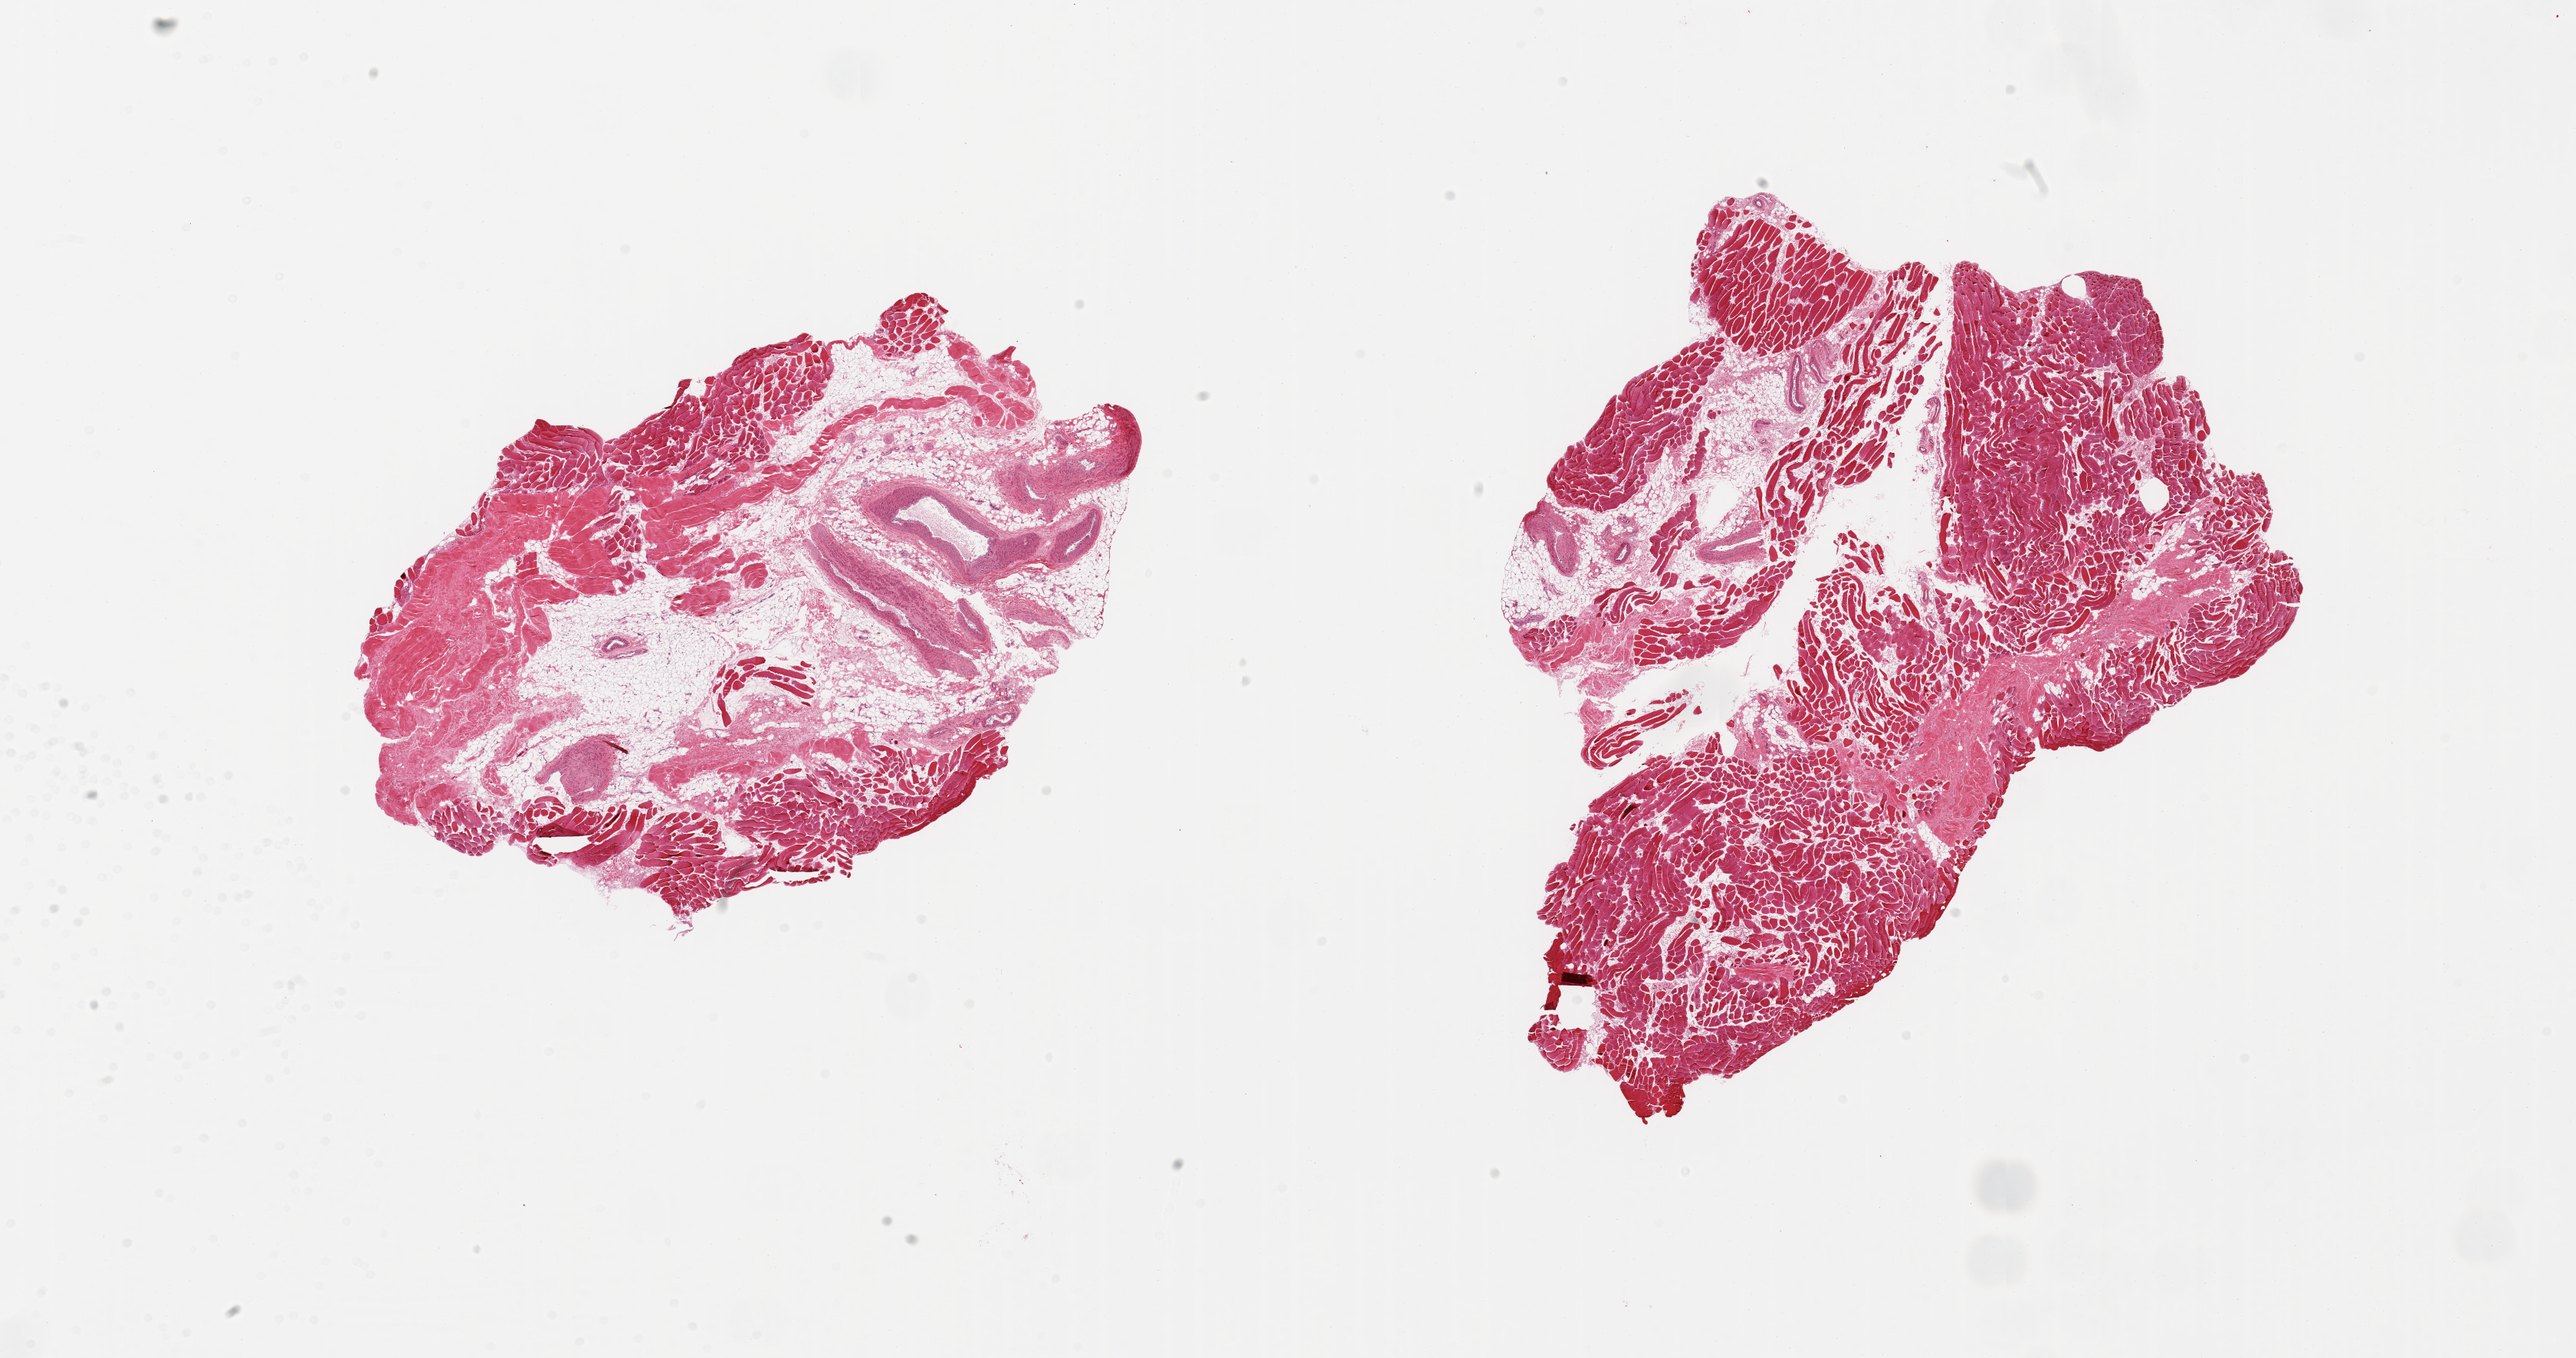
Digitized haematoxylin and eosin-stained section, brightfield — shown as a low-resolution overview of the whole scanned area (about 26.6 x 14.0 mm); PAXgene-fixed paraffin-embedded (PFPE) section; section of skeletal muscle (target tissue); tissue donor sample. Donor sex: male.
* reviewer comment on this tissue sample: 2 pieces: 1 with 80%fat, 10% co-llagen, 10% muscle; other has 80% muscle, 10% collagen, 10% fat